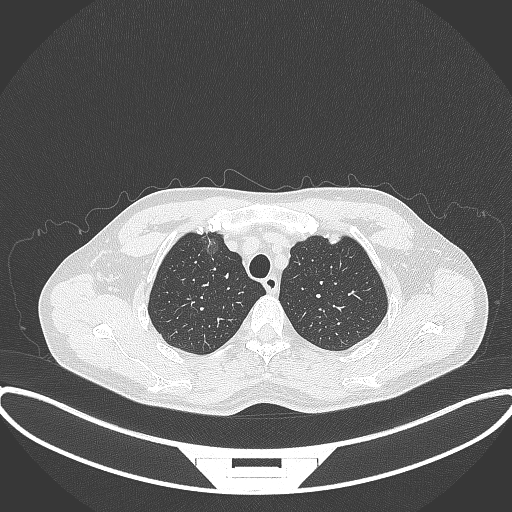
Chest CT, one axial slice; position 304 of 395 along the scan axis; reconstruction kernel B70f; 120 kVp; lung window (W 1500 / L -600 HU); 1 mm slice thickness; 512 × 512 image matrix, field of view 424 × 424 mm. Male patient, age 60 years. From the clinical record (not read from this slice): clinical TNM (as recorded): T1c N0 M0.
Outlined on this slice (bounding box drawn by a radiologist):
- lung tumour (recorded histology: adenocarcinoma): box from (x=204, y=230) to (x=224, y=267) px